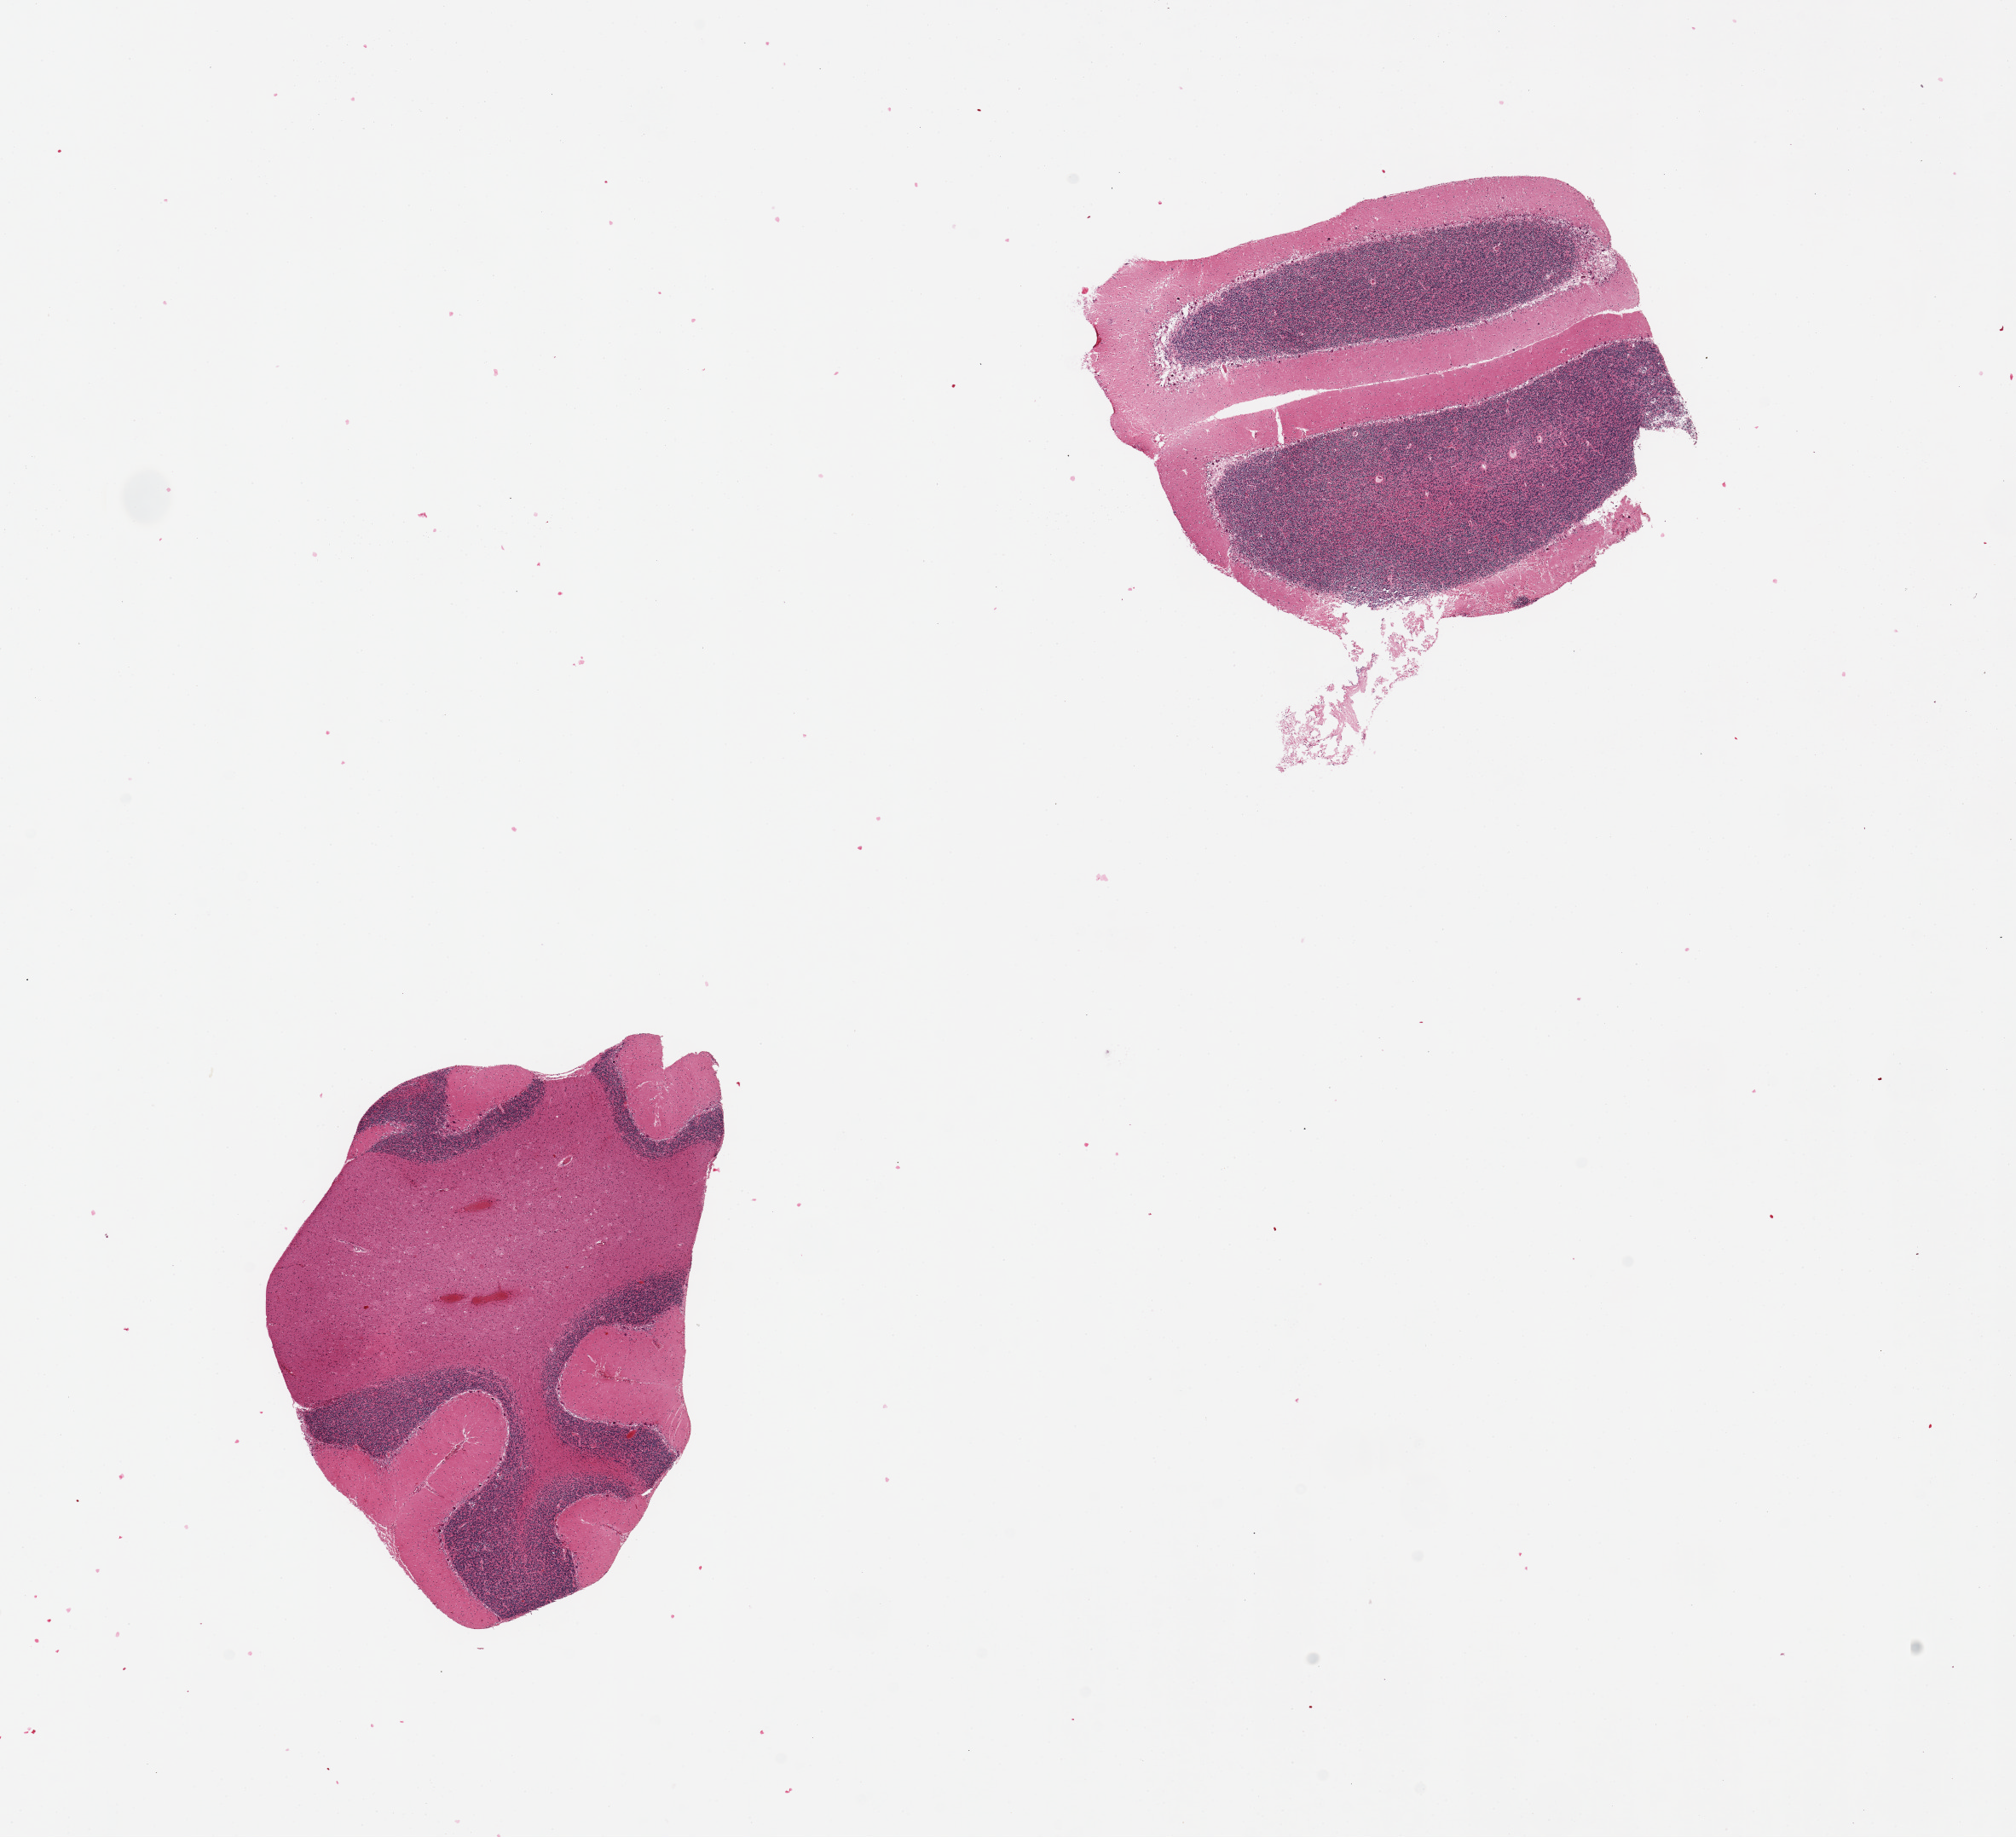
Whole-slide image, hematoxylin and eosin (H&E) stain, brightfield, a low-resolution overview of the entire scanned area, about 18.7 x 17.0 mm (from a 20x scan), PAXgene-fixed, paraffin-embedded tissue, section of cerebellum (target tissue), tissue donor sample. Donor: male.
Review note (as recorded): 2 pieces 6 x 4 and 5 x 4 mm.